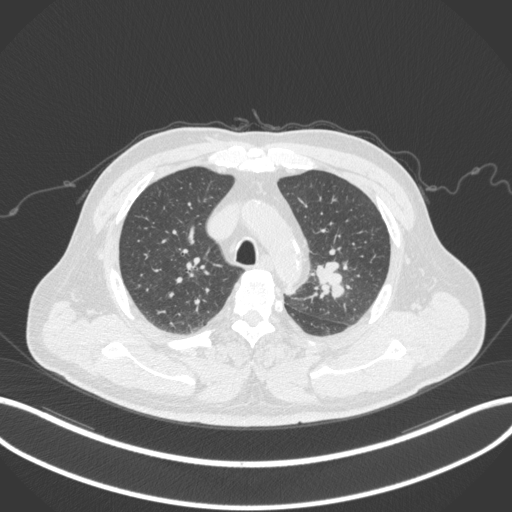
Chest CT, one axial slice; position 228 of 286 along the scan axis; 120 kVp; lung window (W 1500 / L -600 HU); 1 mm slice thickness; 512 × 512 image matrix, field of view 400 × 400 mm. Male patient, age 67 years. Case-level facts recorded for this patient, not image findings: clinical TNM (as recorded): T2a N1 M0; histopathological grade: G3.
Structures marked on this image (bounding box drawn by a radiologist):
- lung tumour (recorded histology: adenocarcinoma): bounding box (x1, y1, x2, y2) in pixels: (311, 254, 352, 304)